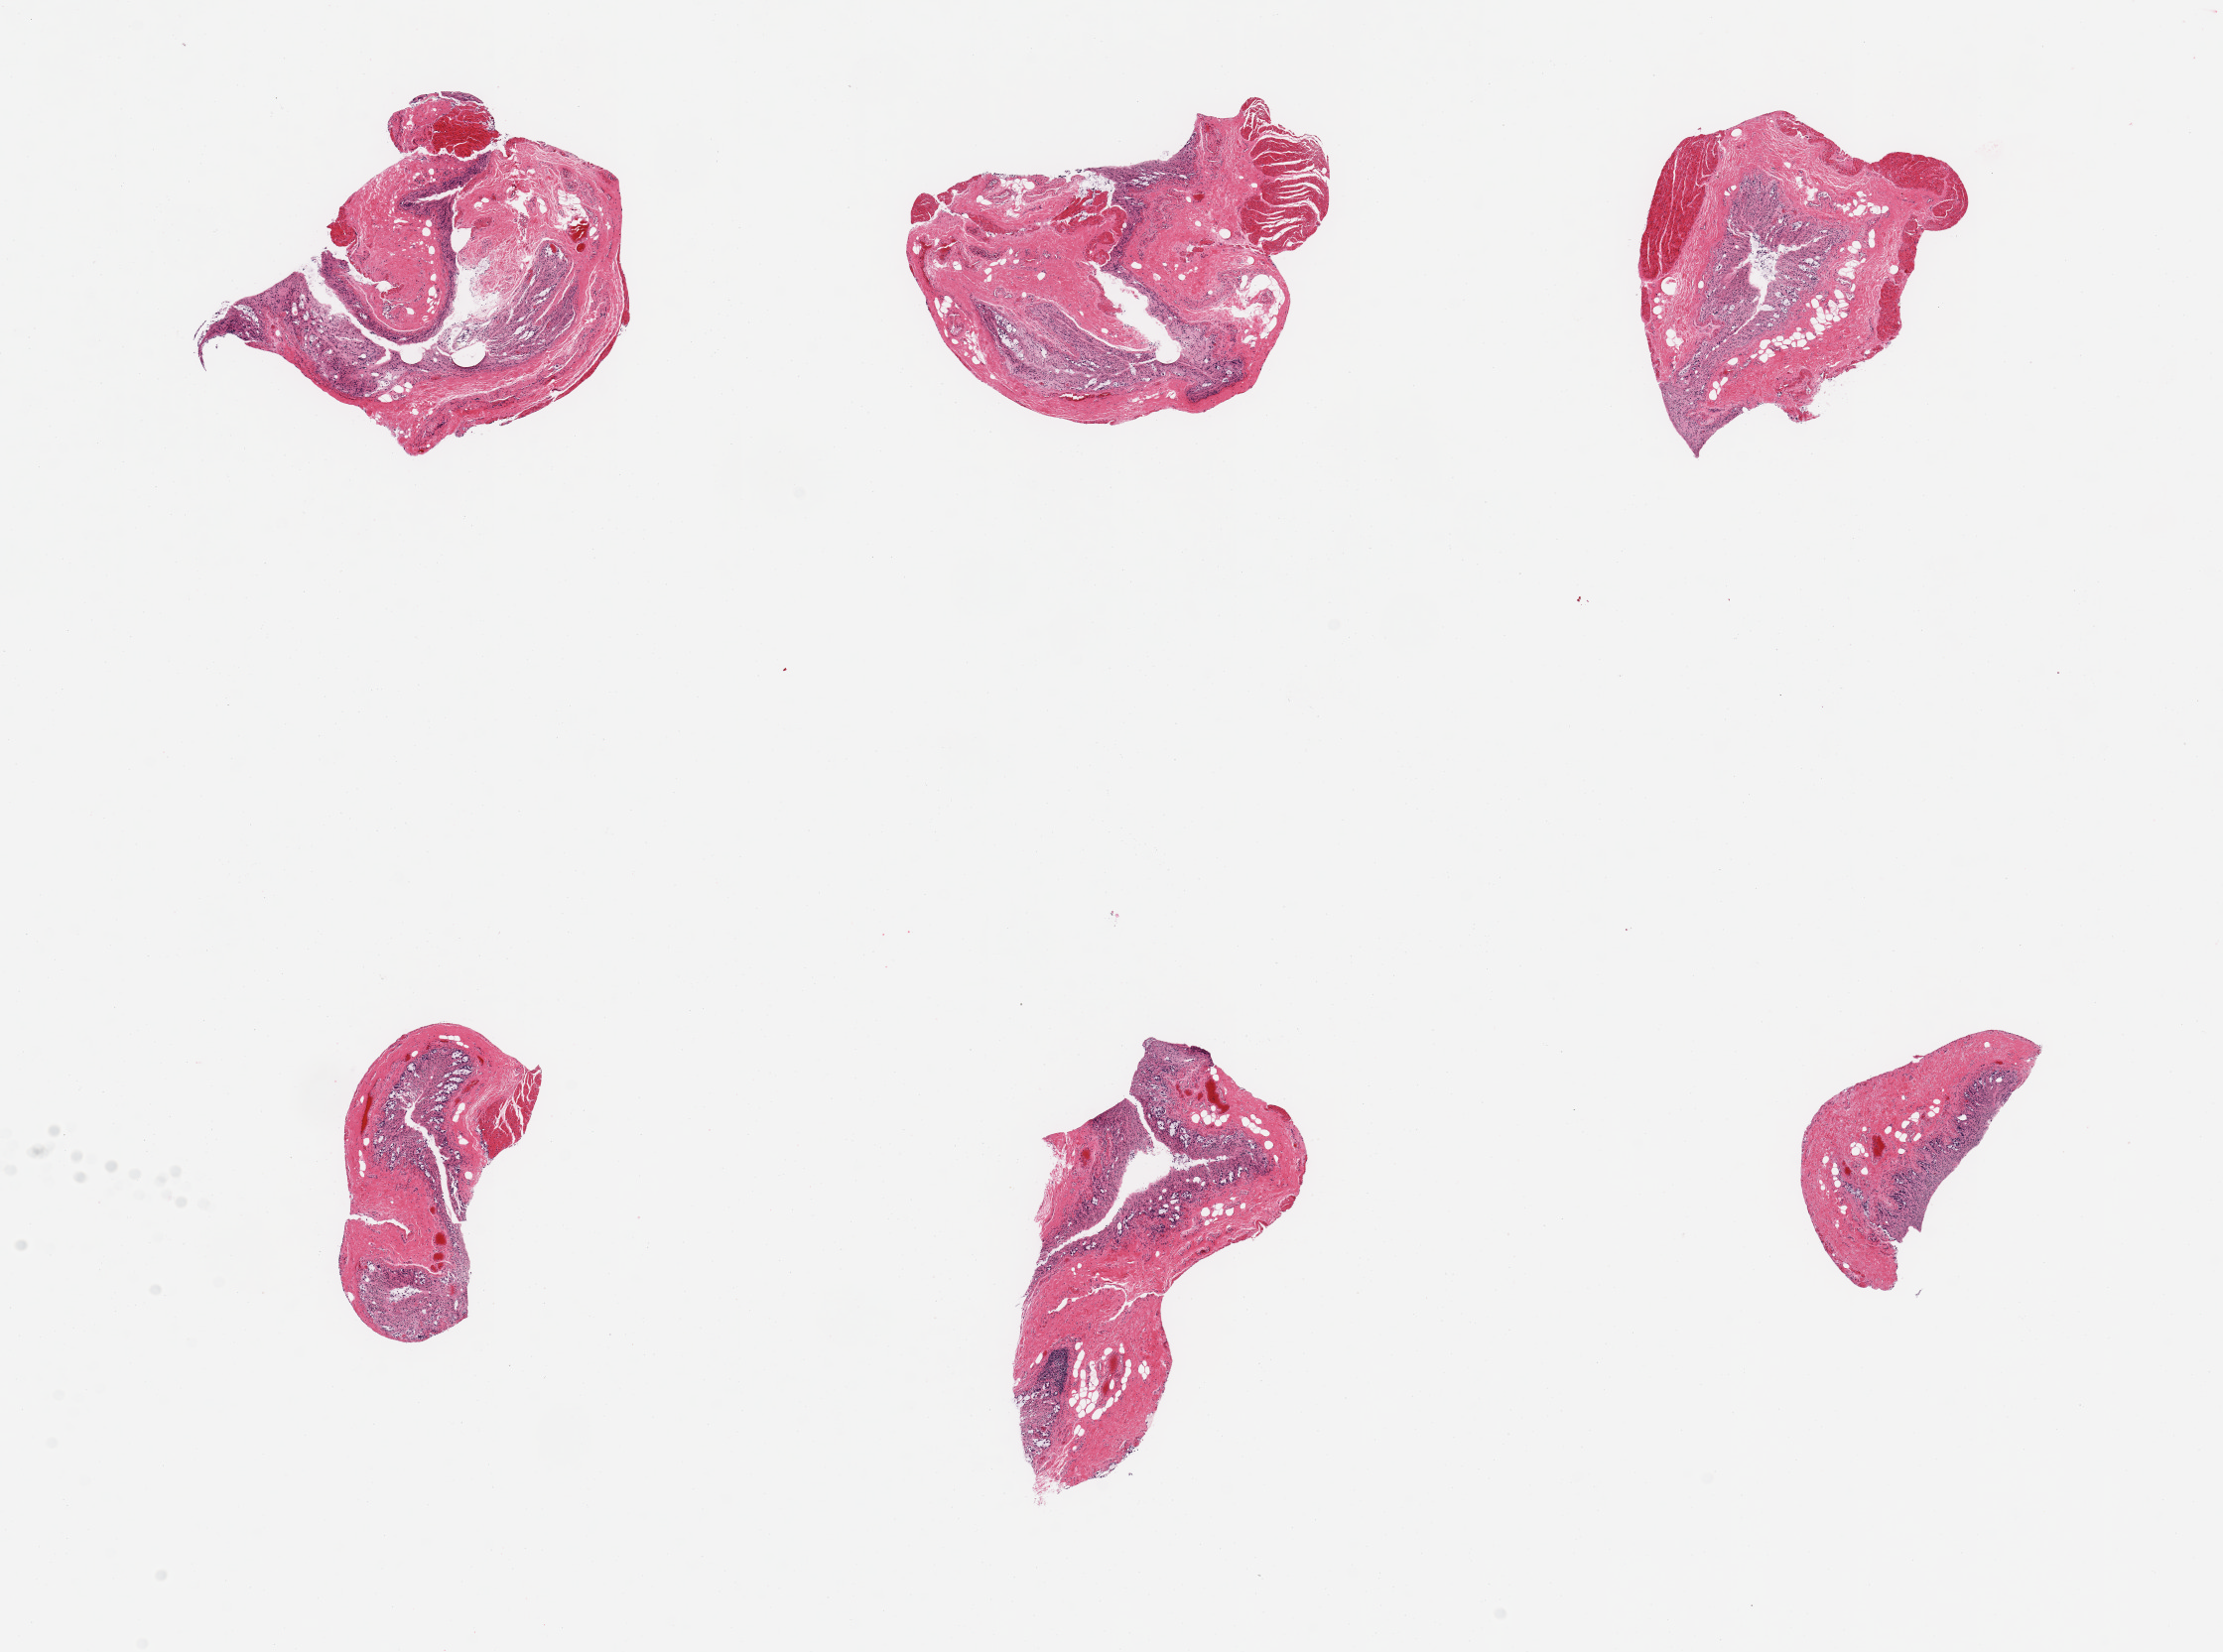
Digitized haematoxylin and eosin-stained section, brightfield — shown as a low-resolution overview of the whole scanned area (about 17.7 x 13.2 mm, acquisition: 20x scan). PAXgene-fixed paraffin-embedded (PFPE) section. Target tissue: sigmoid colon. Donor tissue sample. Male donor.
* reviewer comment on this tissue sample: 6 pieces, minimal target muscularis, mainly autolyzed mucosa and stroma